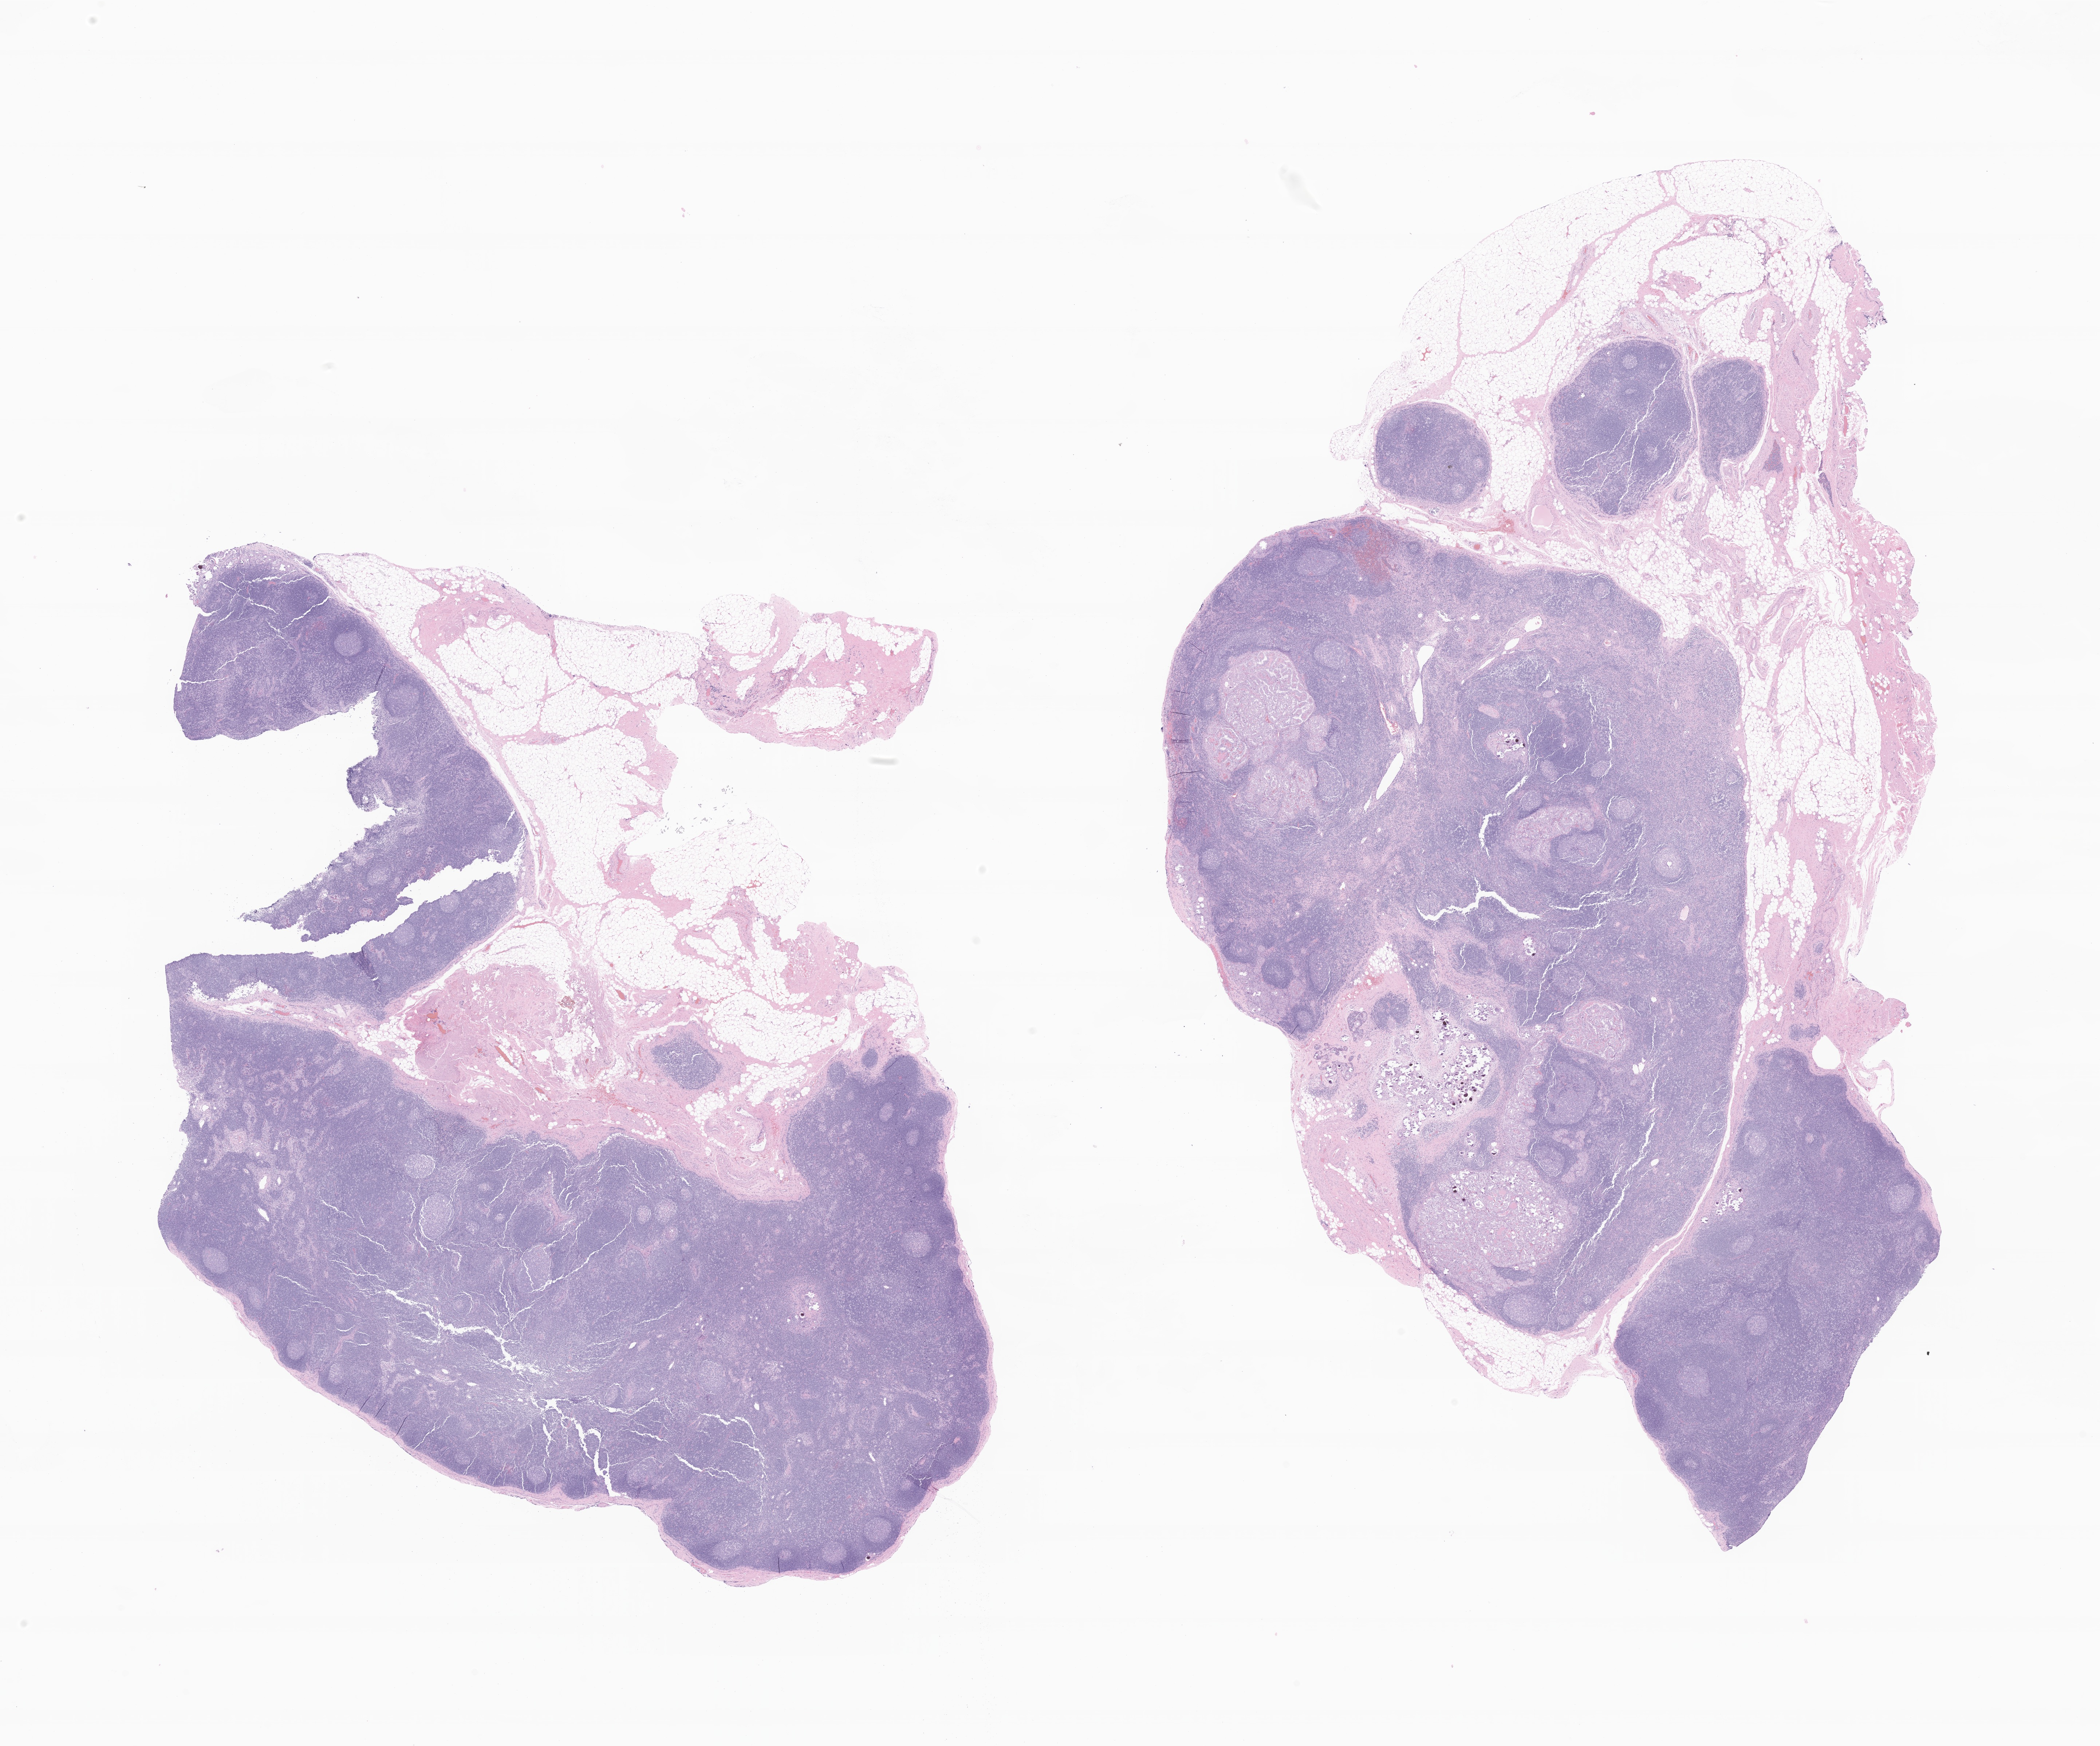
H&E whole-slide image of tumor tissue from the thyroid — shown as a low-resolution overview of the whole scanned area (about 24.3 x 20.2 mm). Formalin-fixed, paraffin-embedded (FFPE) tissue. Female patient, age 219 months (18 years 3 months).
Recorded diagnosis: Papillary carcinoma, NOS.